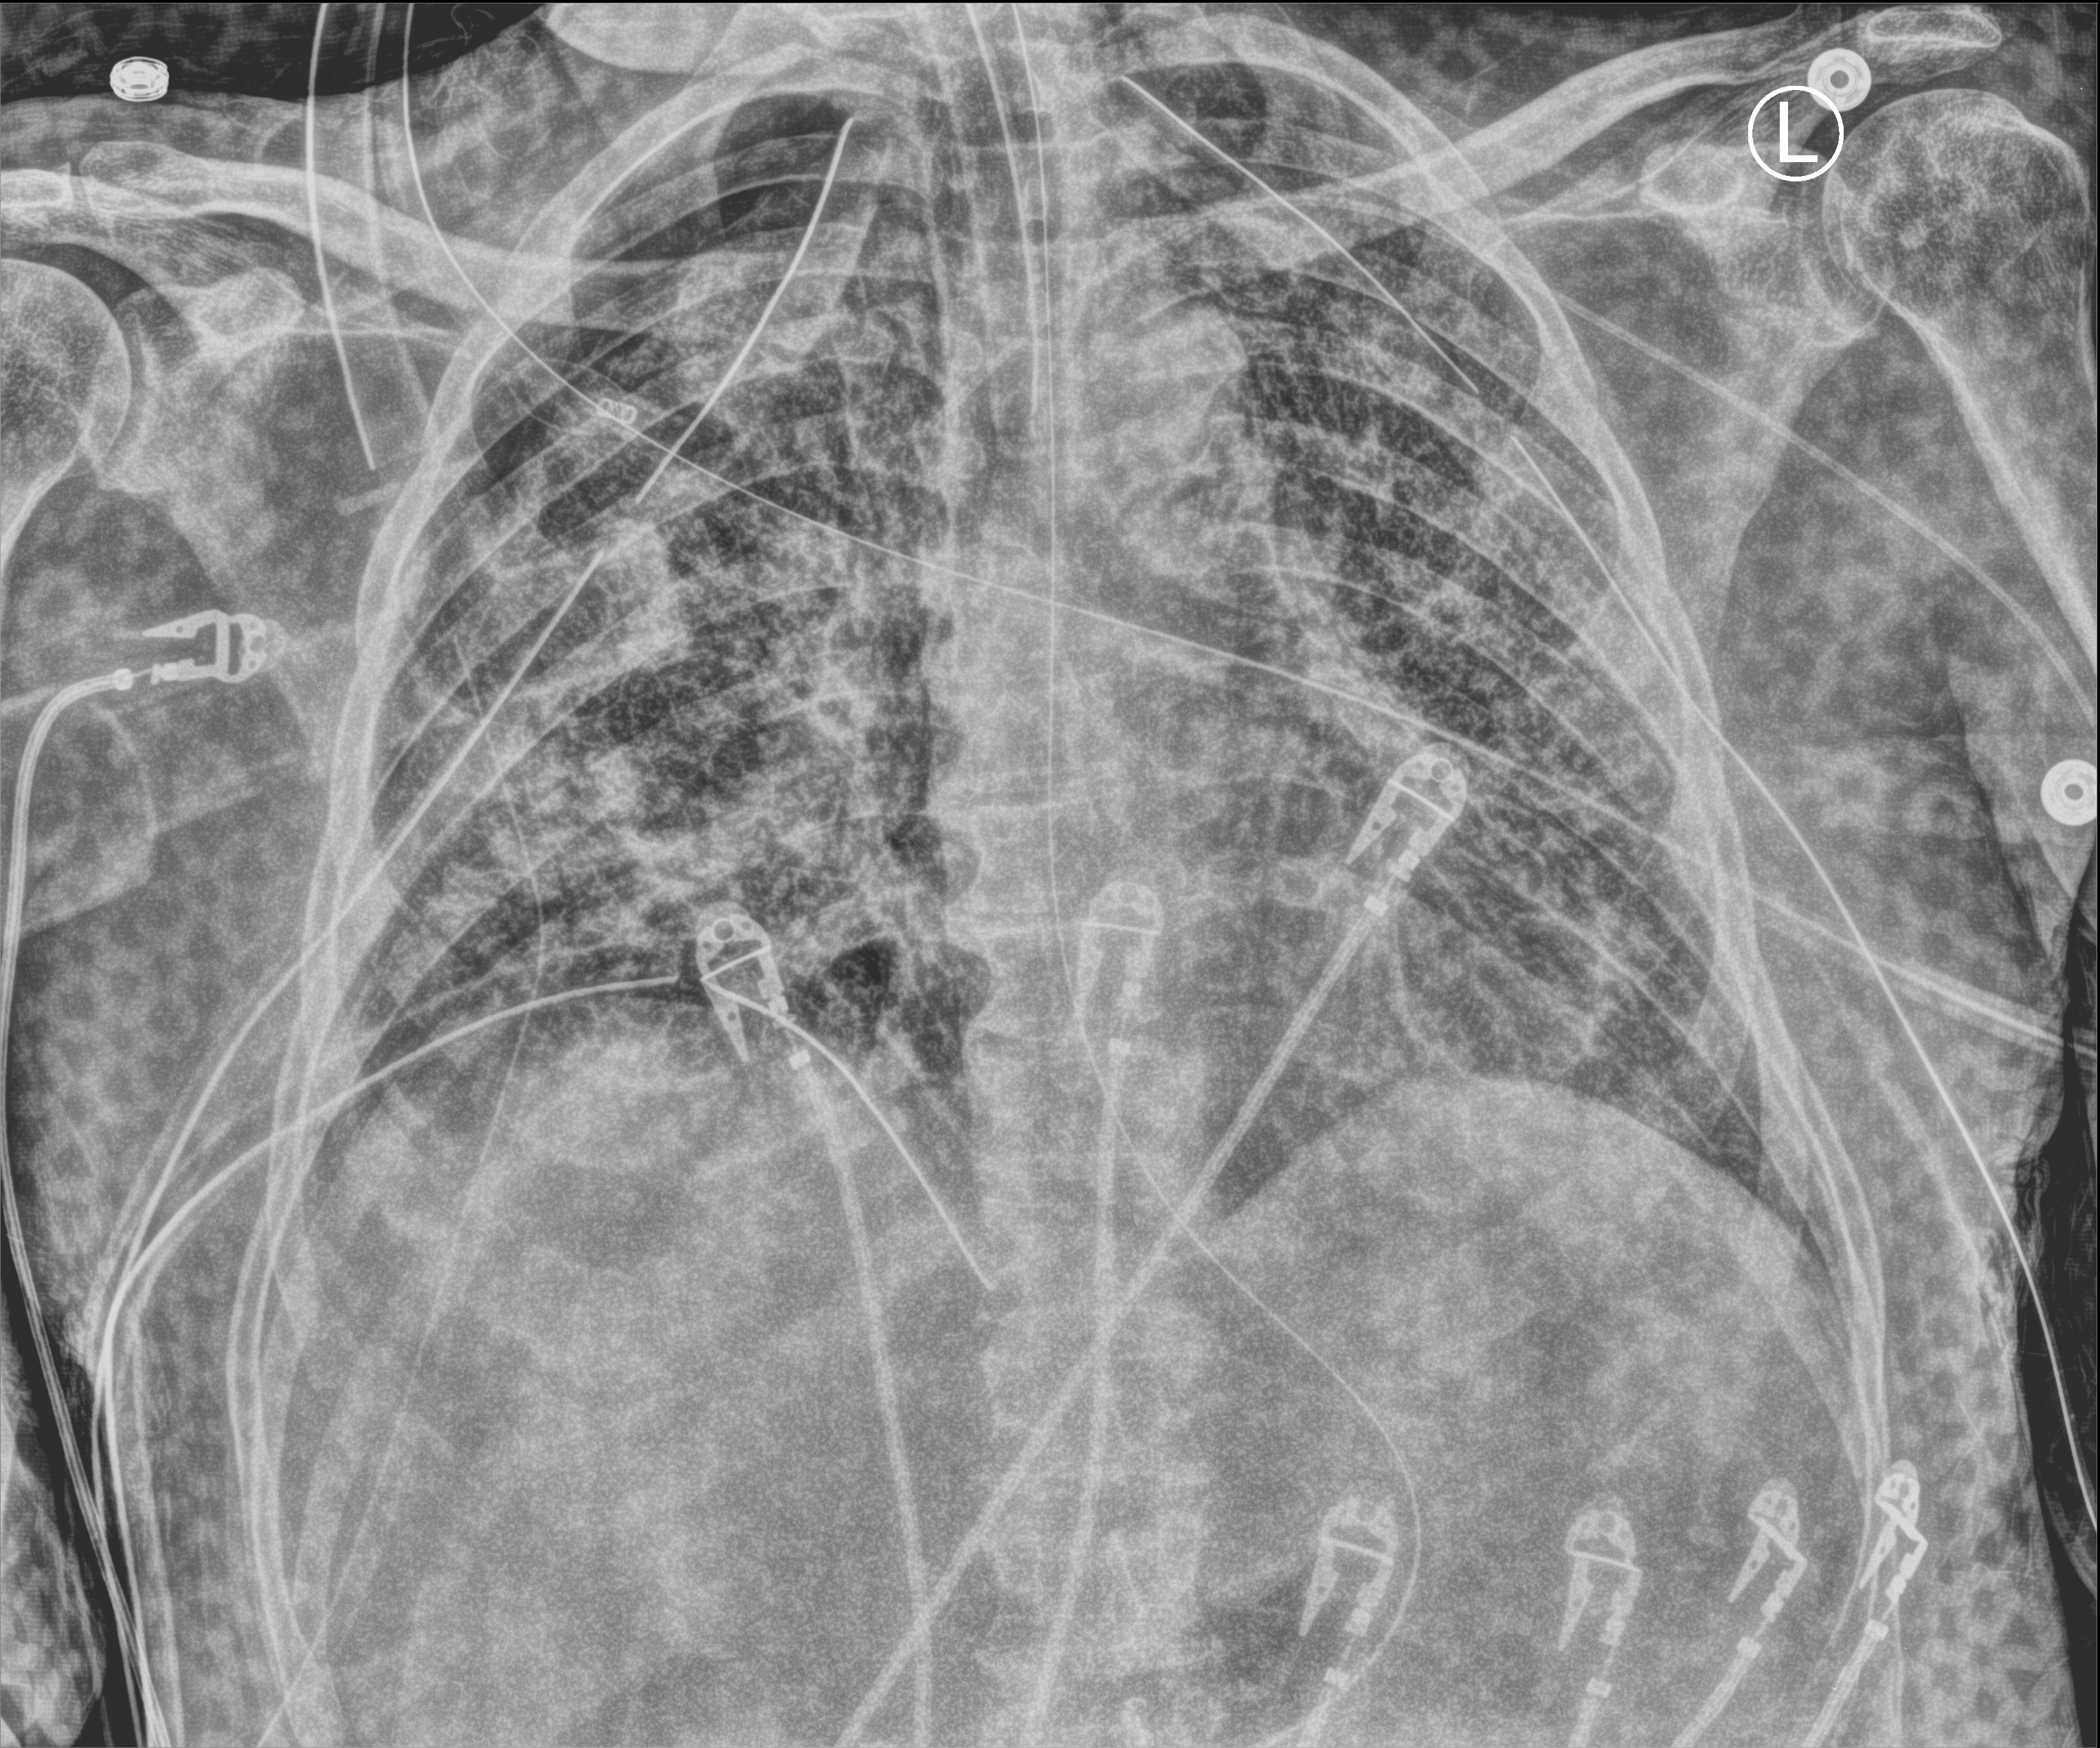
Chest X-ray (portable). Male patient hospitalised with COVID-19, age 18–59 years.
From the hospital-stay record, not from the radiograph (when in the stay this image was taken is not recorded): admitted to intensive care during this hospital stay: yes; diabetes (admission record): no; mechanically ventilated during this hospital stay: yes.